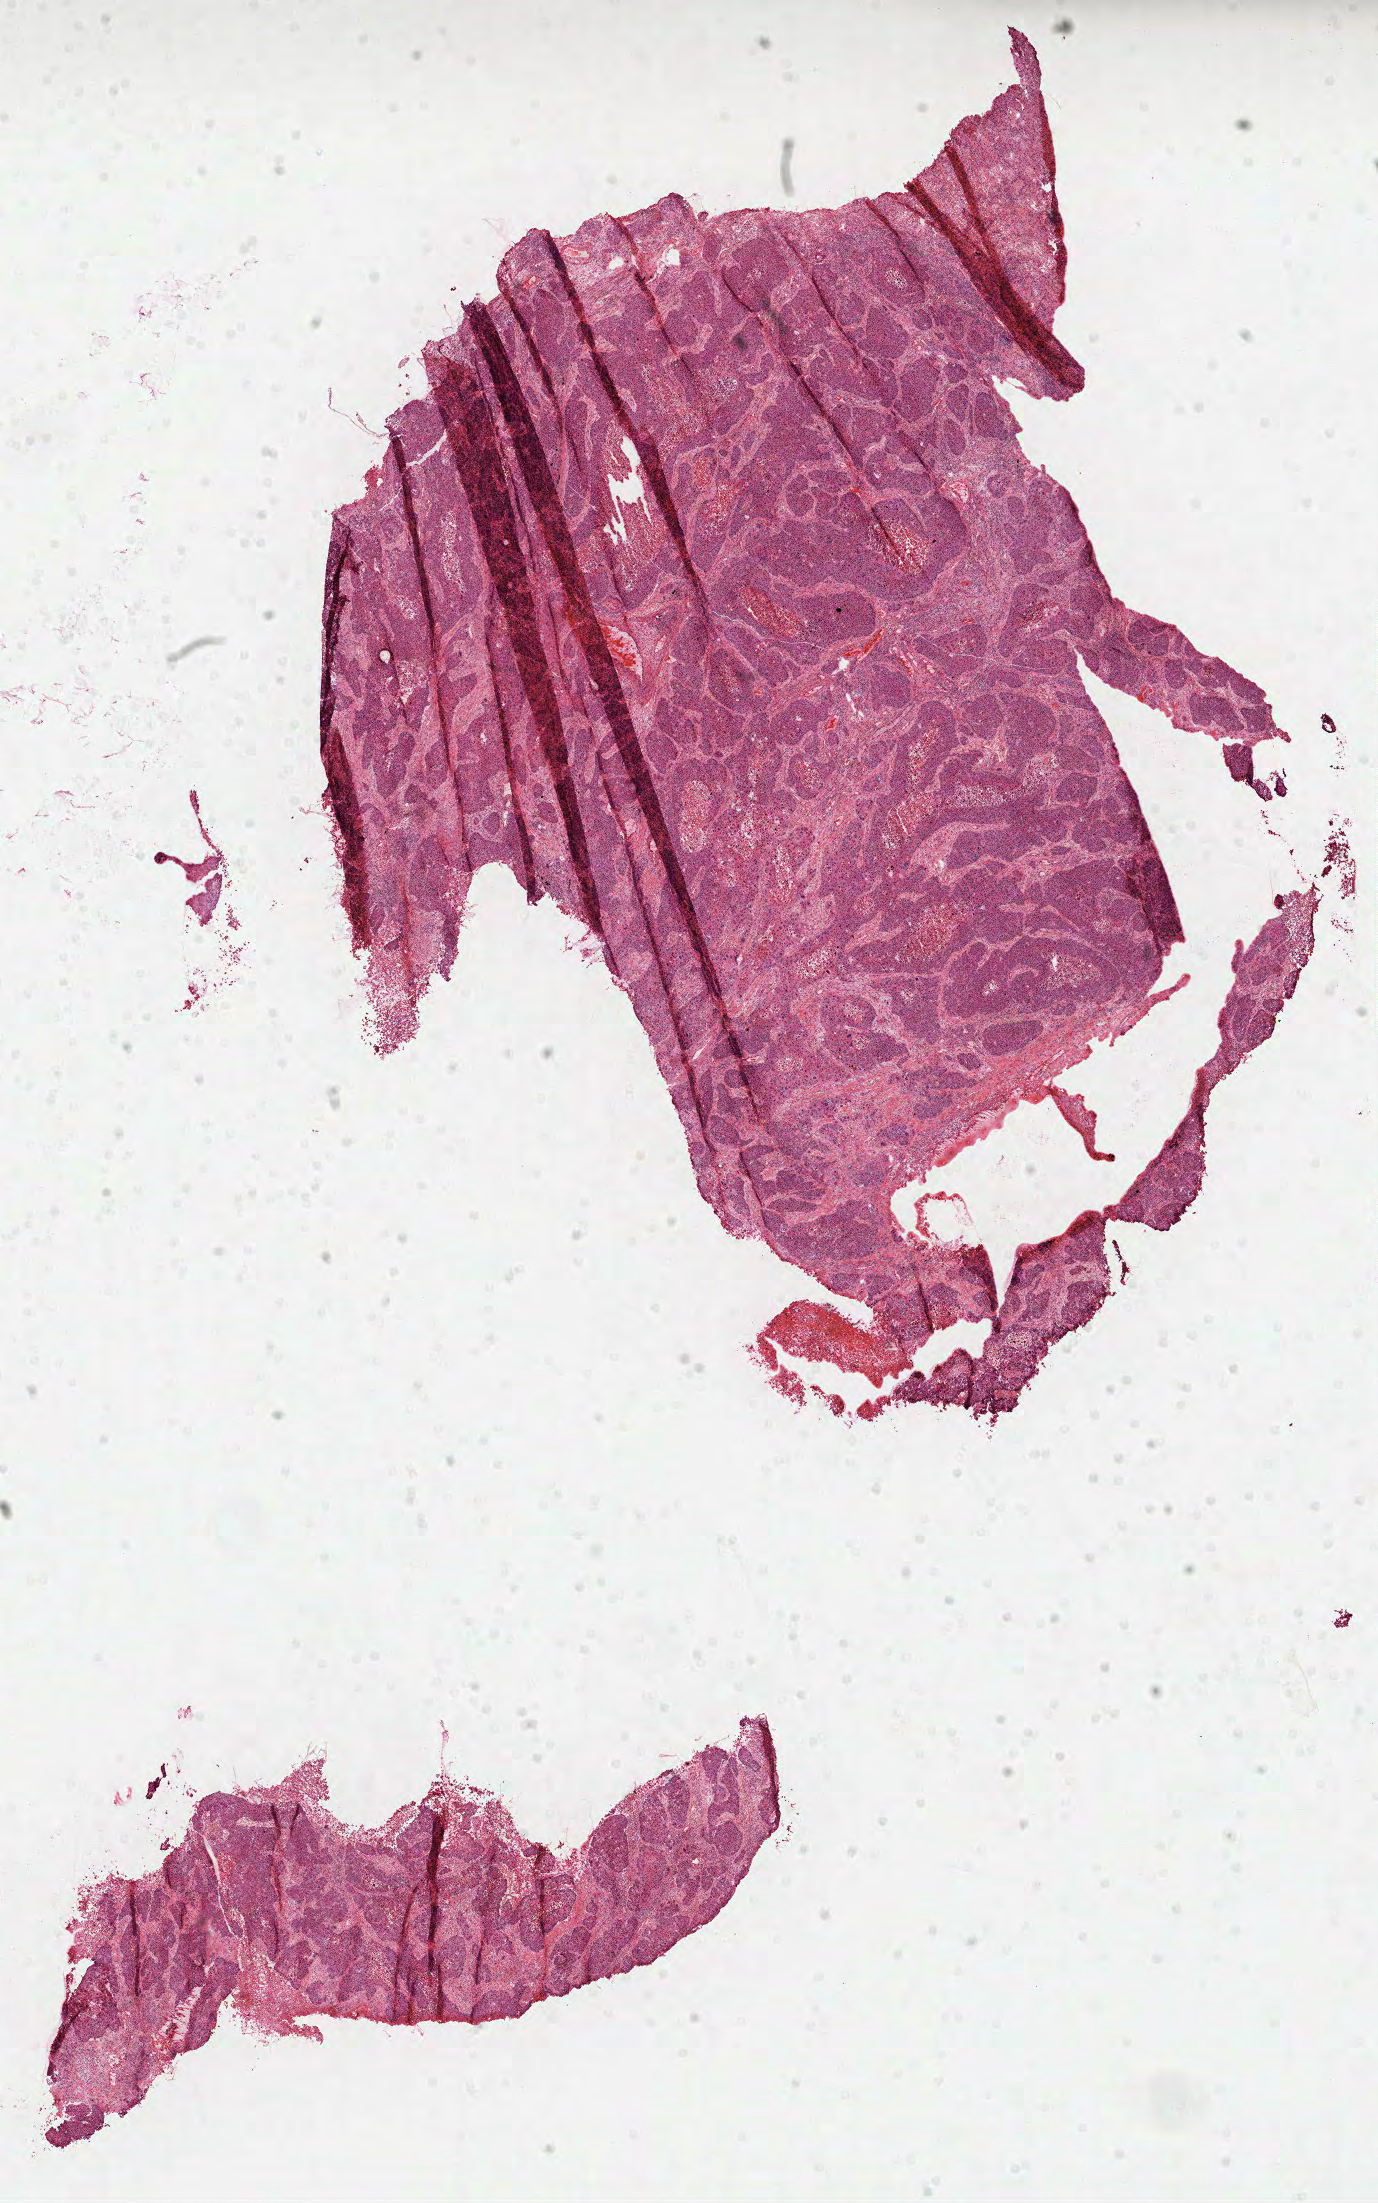
Whole-slide histology image, Hematoxylin and eosin (H&E) stained, low-resolution overview of the scanned area, about 11.1 x 17.8 mm (slide scanned at 40x), formalin-fixed paraffin-embedded (FFPE) diagnostic section, sample: primary tumour, lung. Male patient; age at initial diagnosis 66 years.
Laterality: left. AJCC pathologic stage: IB. Histologic diagnosis: Squamous cell carcinoma, NOS.